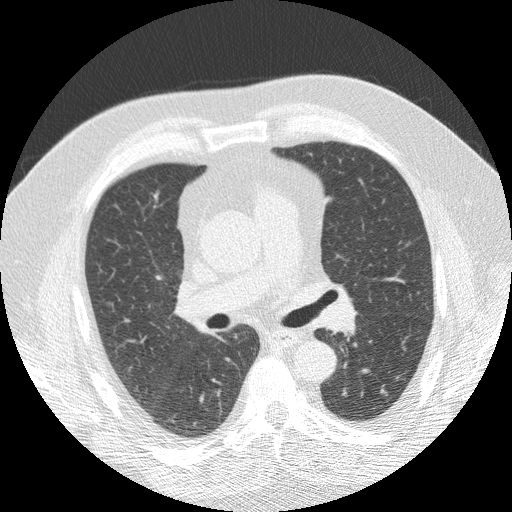
Chest CT (low-dose screening protocol), one axial image; baseline screening round; lung window (W 1500 / L -600 HU); 2.5 mm slice thickness; standard (soft-tissue) reconstruction kernel (STANDARD). Male, age 69 years at enrolment.
Expert-annotated lung lesion, bounding box [x1, y1, x2, y2] px = [368, 373, 402, 411]. No non-calcified nodule or mass ≥4 mm was recorded by the screening reader at this exam. Participant outcome: lung cancer diagnosed 939 days after this screen — squamous cell carcinoma, NOS, left lower lobe, moderately differentiated (G2), stage IA (AJCC 6th edition), 14 mm at pathology.